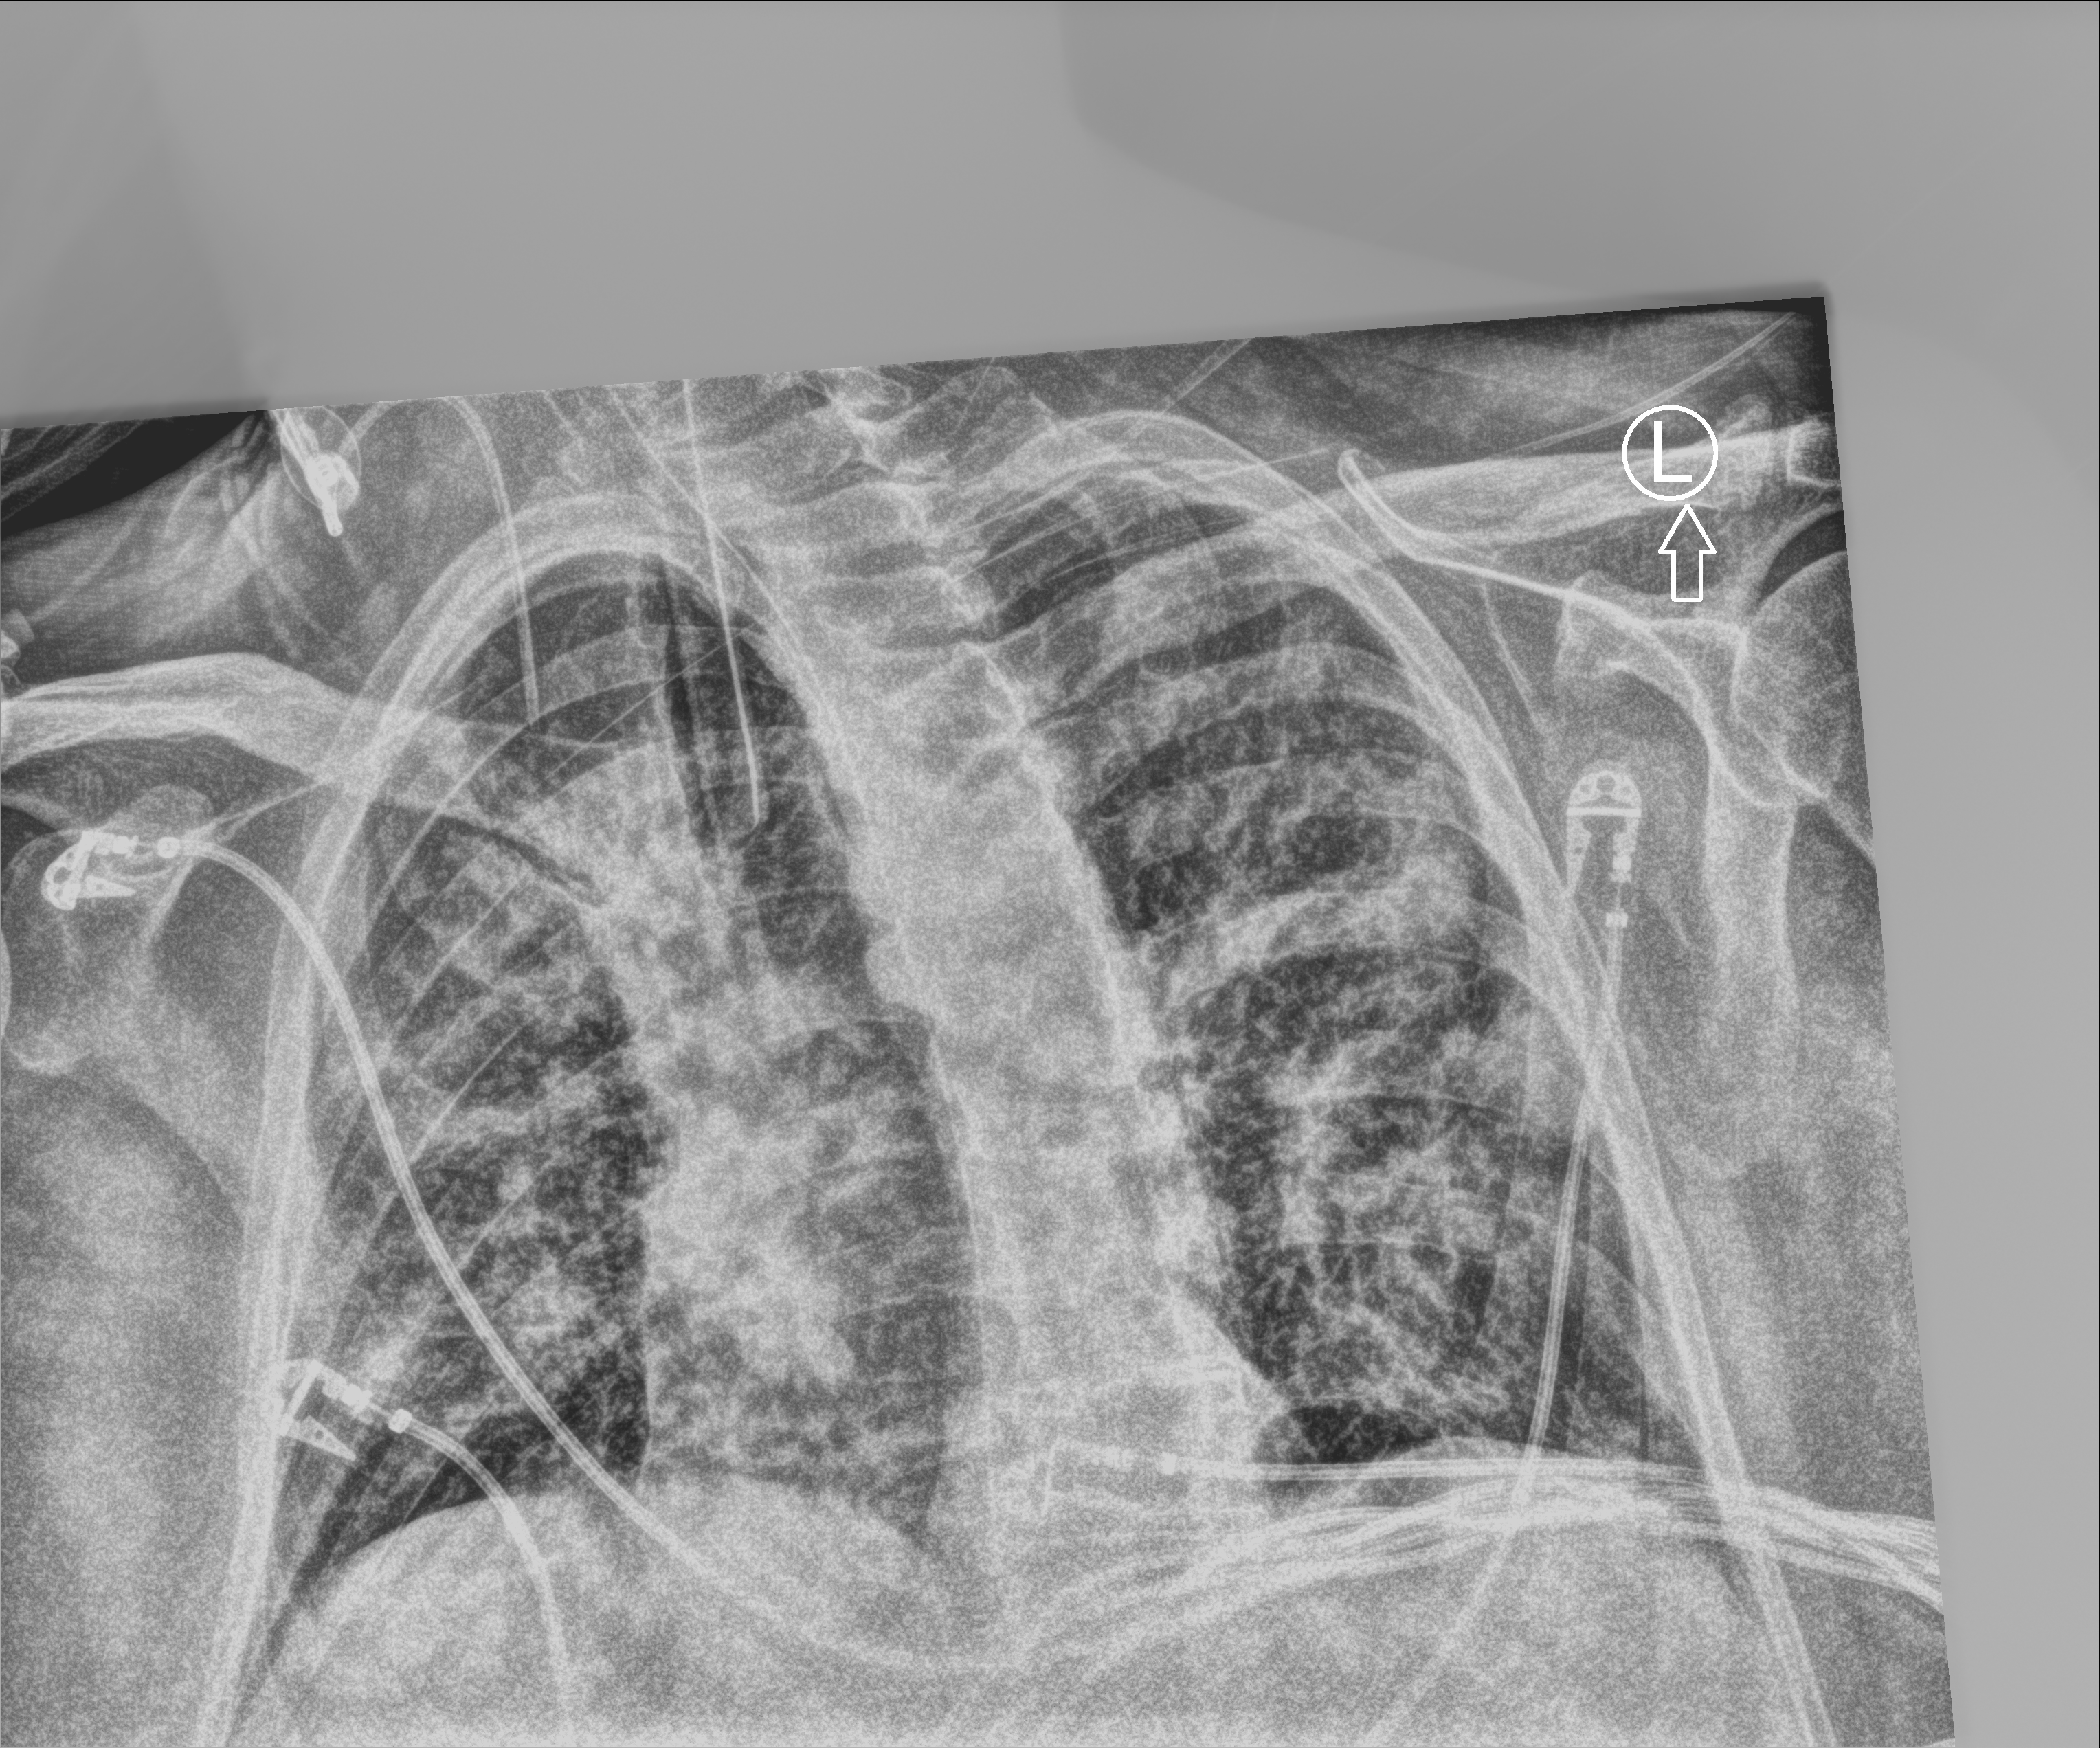
Bedside chest radiograph (computed radiography). Patient hospitalised with COVID-19; male, aged 60–74 years.
From the hospital-stay record, not from the radiograph (when in the stay this image was taken is not recorded):
- admitted to intensive care during this hospital stay: yes
- mechanically ventilated during this hospital stay: yes